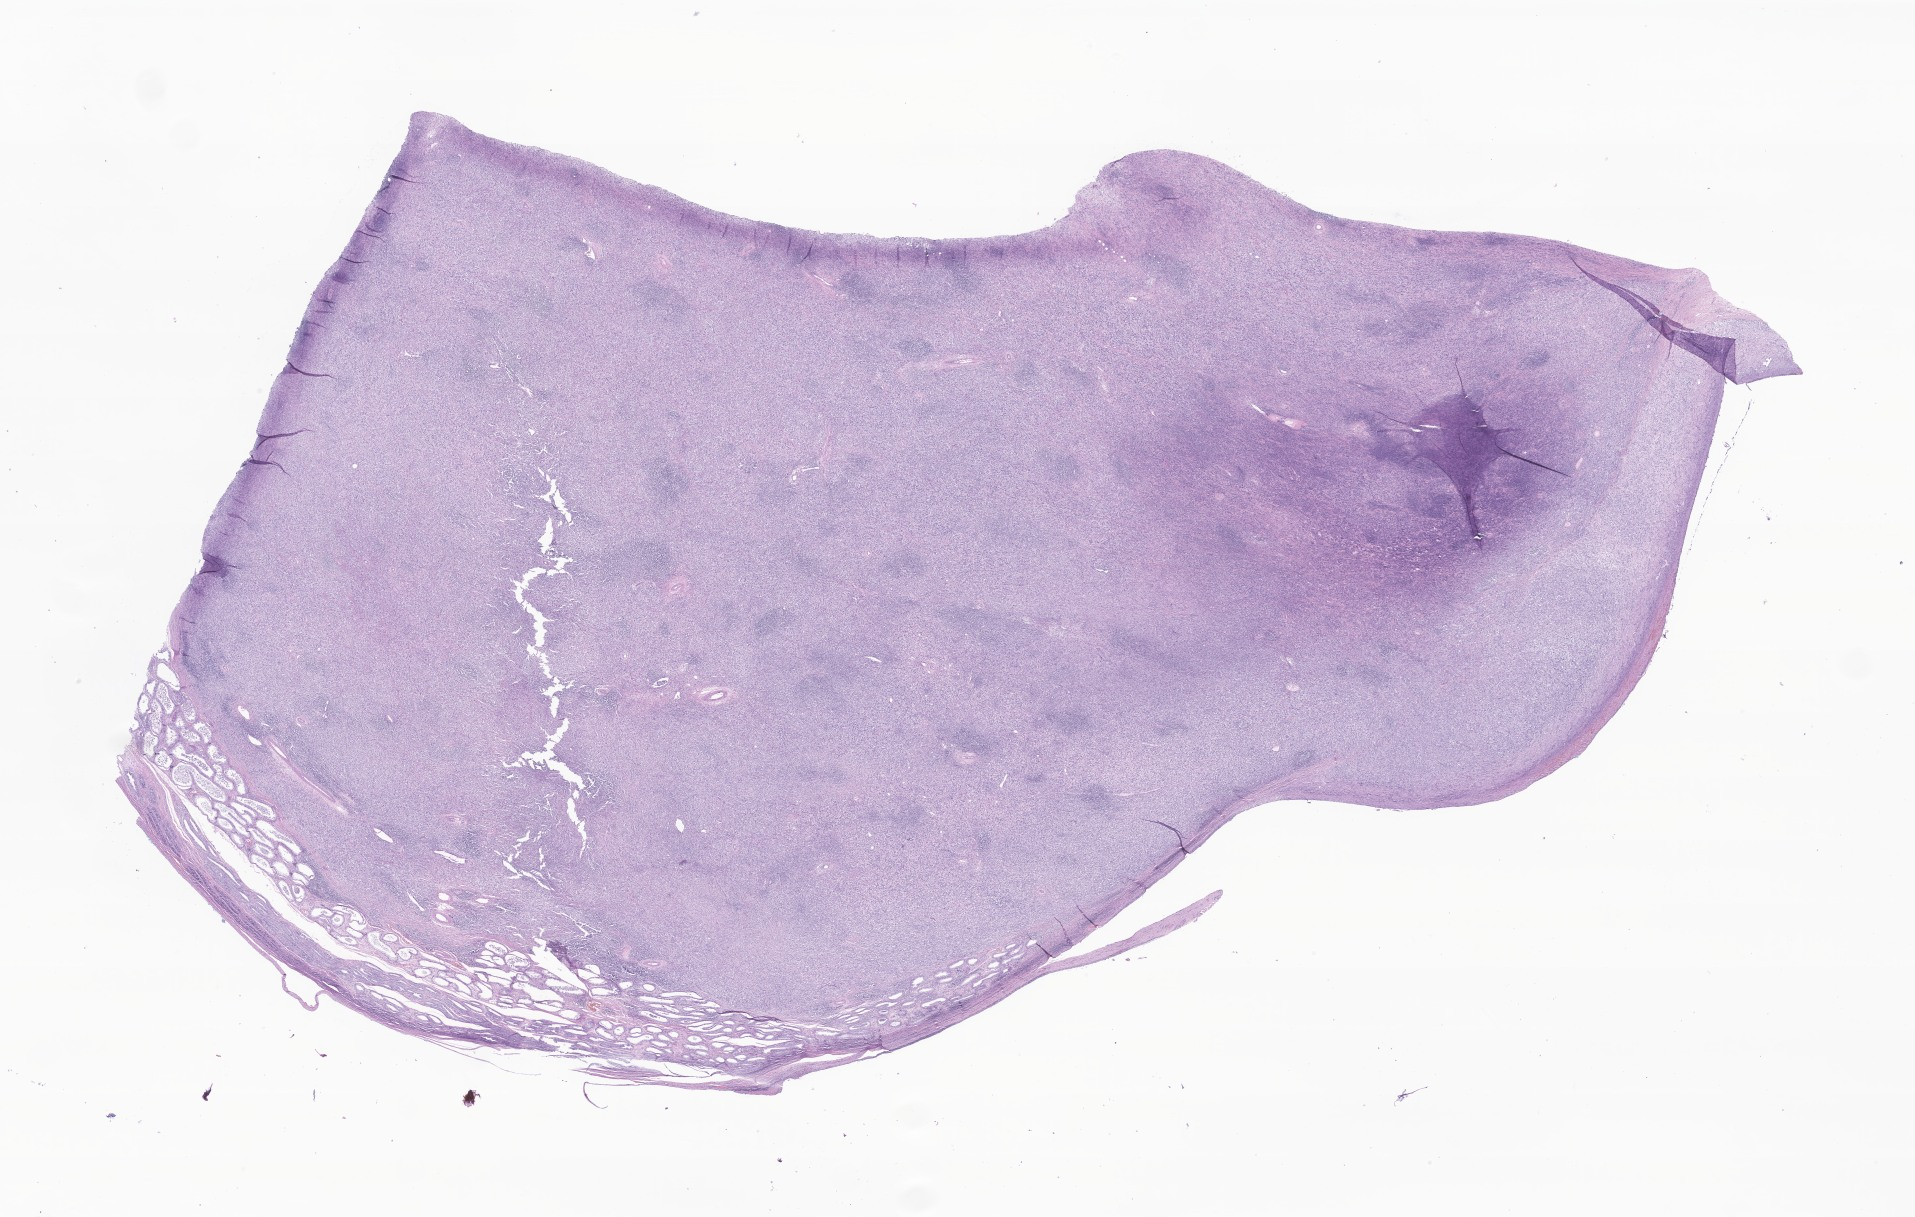
Hematoxylin and eosin (H&E) whole-slide image of tumor tissue from the testis, a low-resolution overview of the entire scanned area, about 32.3 x 20.5 mm, formalin-fixed, paraffin-embedded (FFPE) tissue. Male patient, age 217 months (18 years 1 month).
• diagnosis (ICD-O-3 morphology term): Rhabdomyosarcoma, NOS